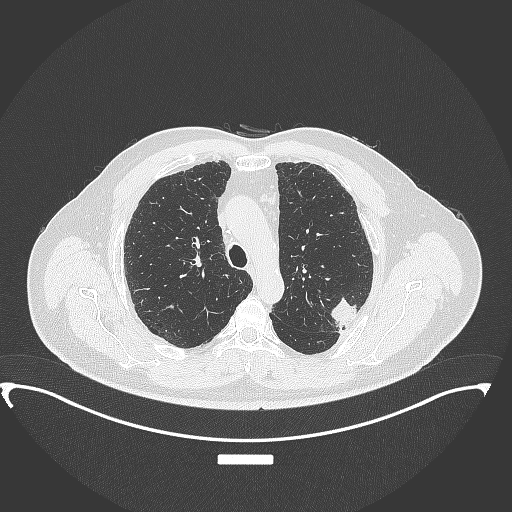
Chest CT, one axial slice; position 261 of 350 along the scan axis; 120 kVp; lung window (W 1500 / L -600 HU); 512 × 512 image matrix. Patient: male, 64 years. From the clinical record (not read from this slice): clinical TNM (as recorded): T1c N1 M1.
Structures marked on this image (rectangle marked by the reading radiologist):
- lung tumour (recorded histology: adenocarcinoma): bounding box (x1, y1, x2, y2) in pixels: (326, 293, 364, 328)